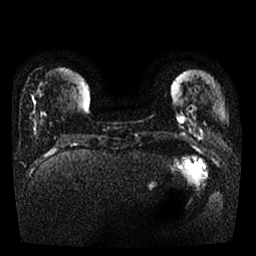
Breast MRI, one axial slice. Position 4 of 25 along the scan axis. Diffusion-weighted series; image 2 of 4 stored at this slice position (different b-values; order by instance number). 1.5 T. 256 × 256 image matrix, field of view 330 × 330 mm. Female patient.
Outlined on this slice (expert manual segmentation):
- tumour on diffusion-weighted imaging: bounding box <176,114,184,124> (left, top, right, bottom; pixels)